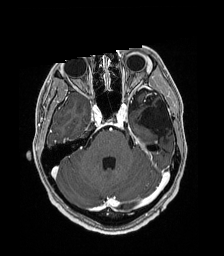
Brain MRI from a brain-tumour surgery series, one axial slice. Slice 126 of 192 in the series (ordered by position). T1-weighted post-contrast. 1 mm slice thickness. 224 × 256 image matrix, field of view 224 × 256 mm. From the clinical record (not read from this slice): histopathology: Low grade glioma; IDH mutation: no; tumour location: Left Parieto-Occipital Intraventricular.
Outlined on this slice (expert manual segmentation):
- previous resection cavity: bounding box (x1, y1, x2, y2) in pixels: (139, 100, 171, 136)